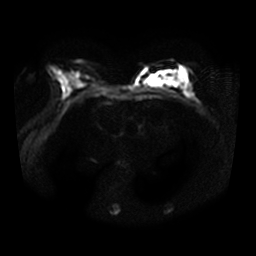
Breast MRI, one axial slice. Position 15 of 32 along the scan axis. Diffusion-weighted series; image 2 of 4 stored at this slice position (different b-values; order by instance number). 3 T. 256 × 256 image matrix, field of view 340 × 340 mm. Female patient.
Annotated regions visible in this slice (manually delineated by an expert):
- tumour on diffusion-weighted imaging: bounding box [x1, y1, x2, y2] px = [144, 70, 179, 87]